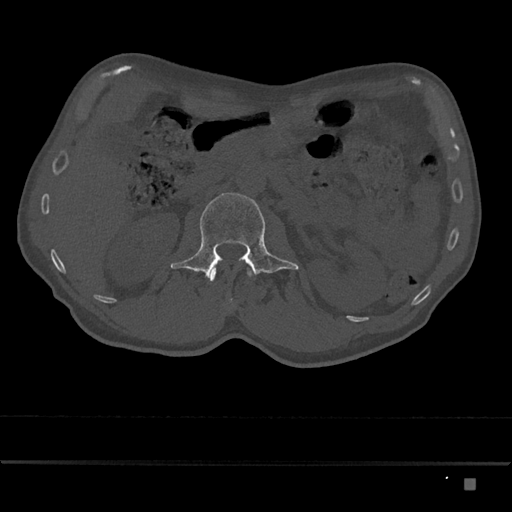
CT including the spine, one axial slice; slice 491 of 797 in the series (ordered by position); bone window (W 1800 / L 400 HU); 512 × 512 image matrix, field of view 390 × 390 mm. Patient: male, 72 years. Case-level facts recorded for this patient, not image findings: primary cancer: prostate.
Structures marked on this image (semi-automatically segmented with operator editing):
- L1 vertebra: box from (x=210, y=267) to (x=252, y=282) px
- L2 vertebra: (x=171, y=193)–(x=299, y=278)